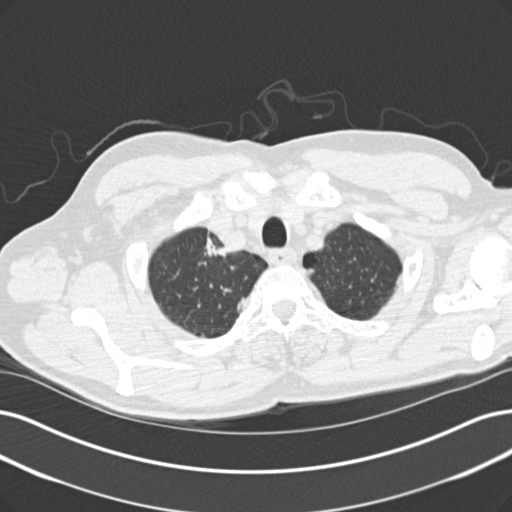
Low-dose screening chest CT, one axial slice. Slice 131 of 152 in the series (ordered by position). Reconstruction kernel B30f. Lung window (W 1500 / L -600 HU). 2 mm slice thickness. 512 × 512 image matrix, field of view 365 × 365 mm.
Outlined on this slice (expert manual segmentation):
- lesion 1 (tumor, upper lobe of right lung): bounding box <204,237,226,257> (left, top, right, bottom; pixels)